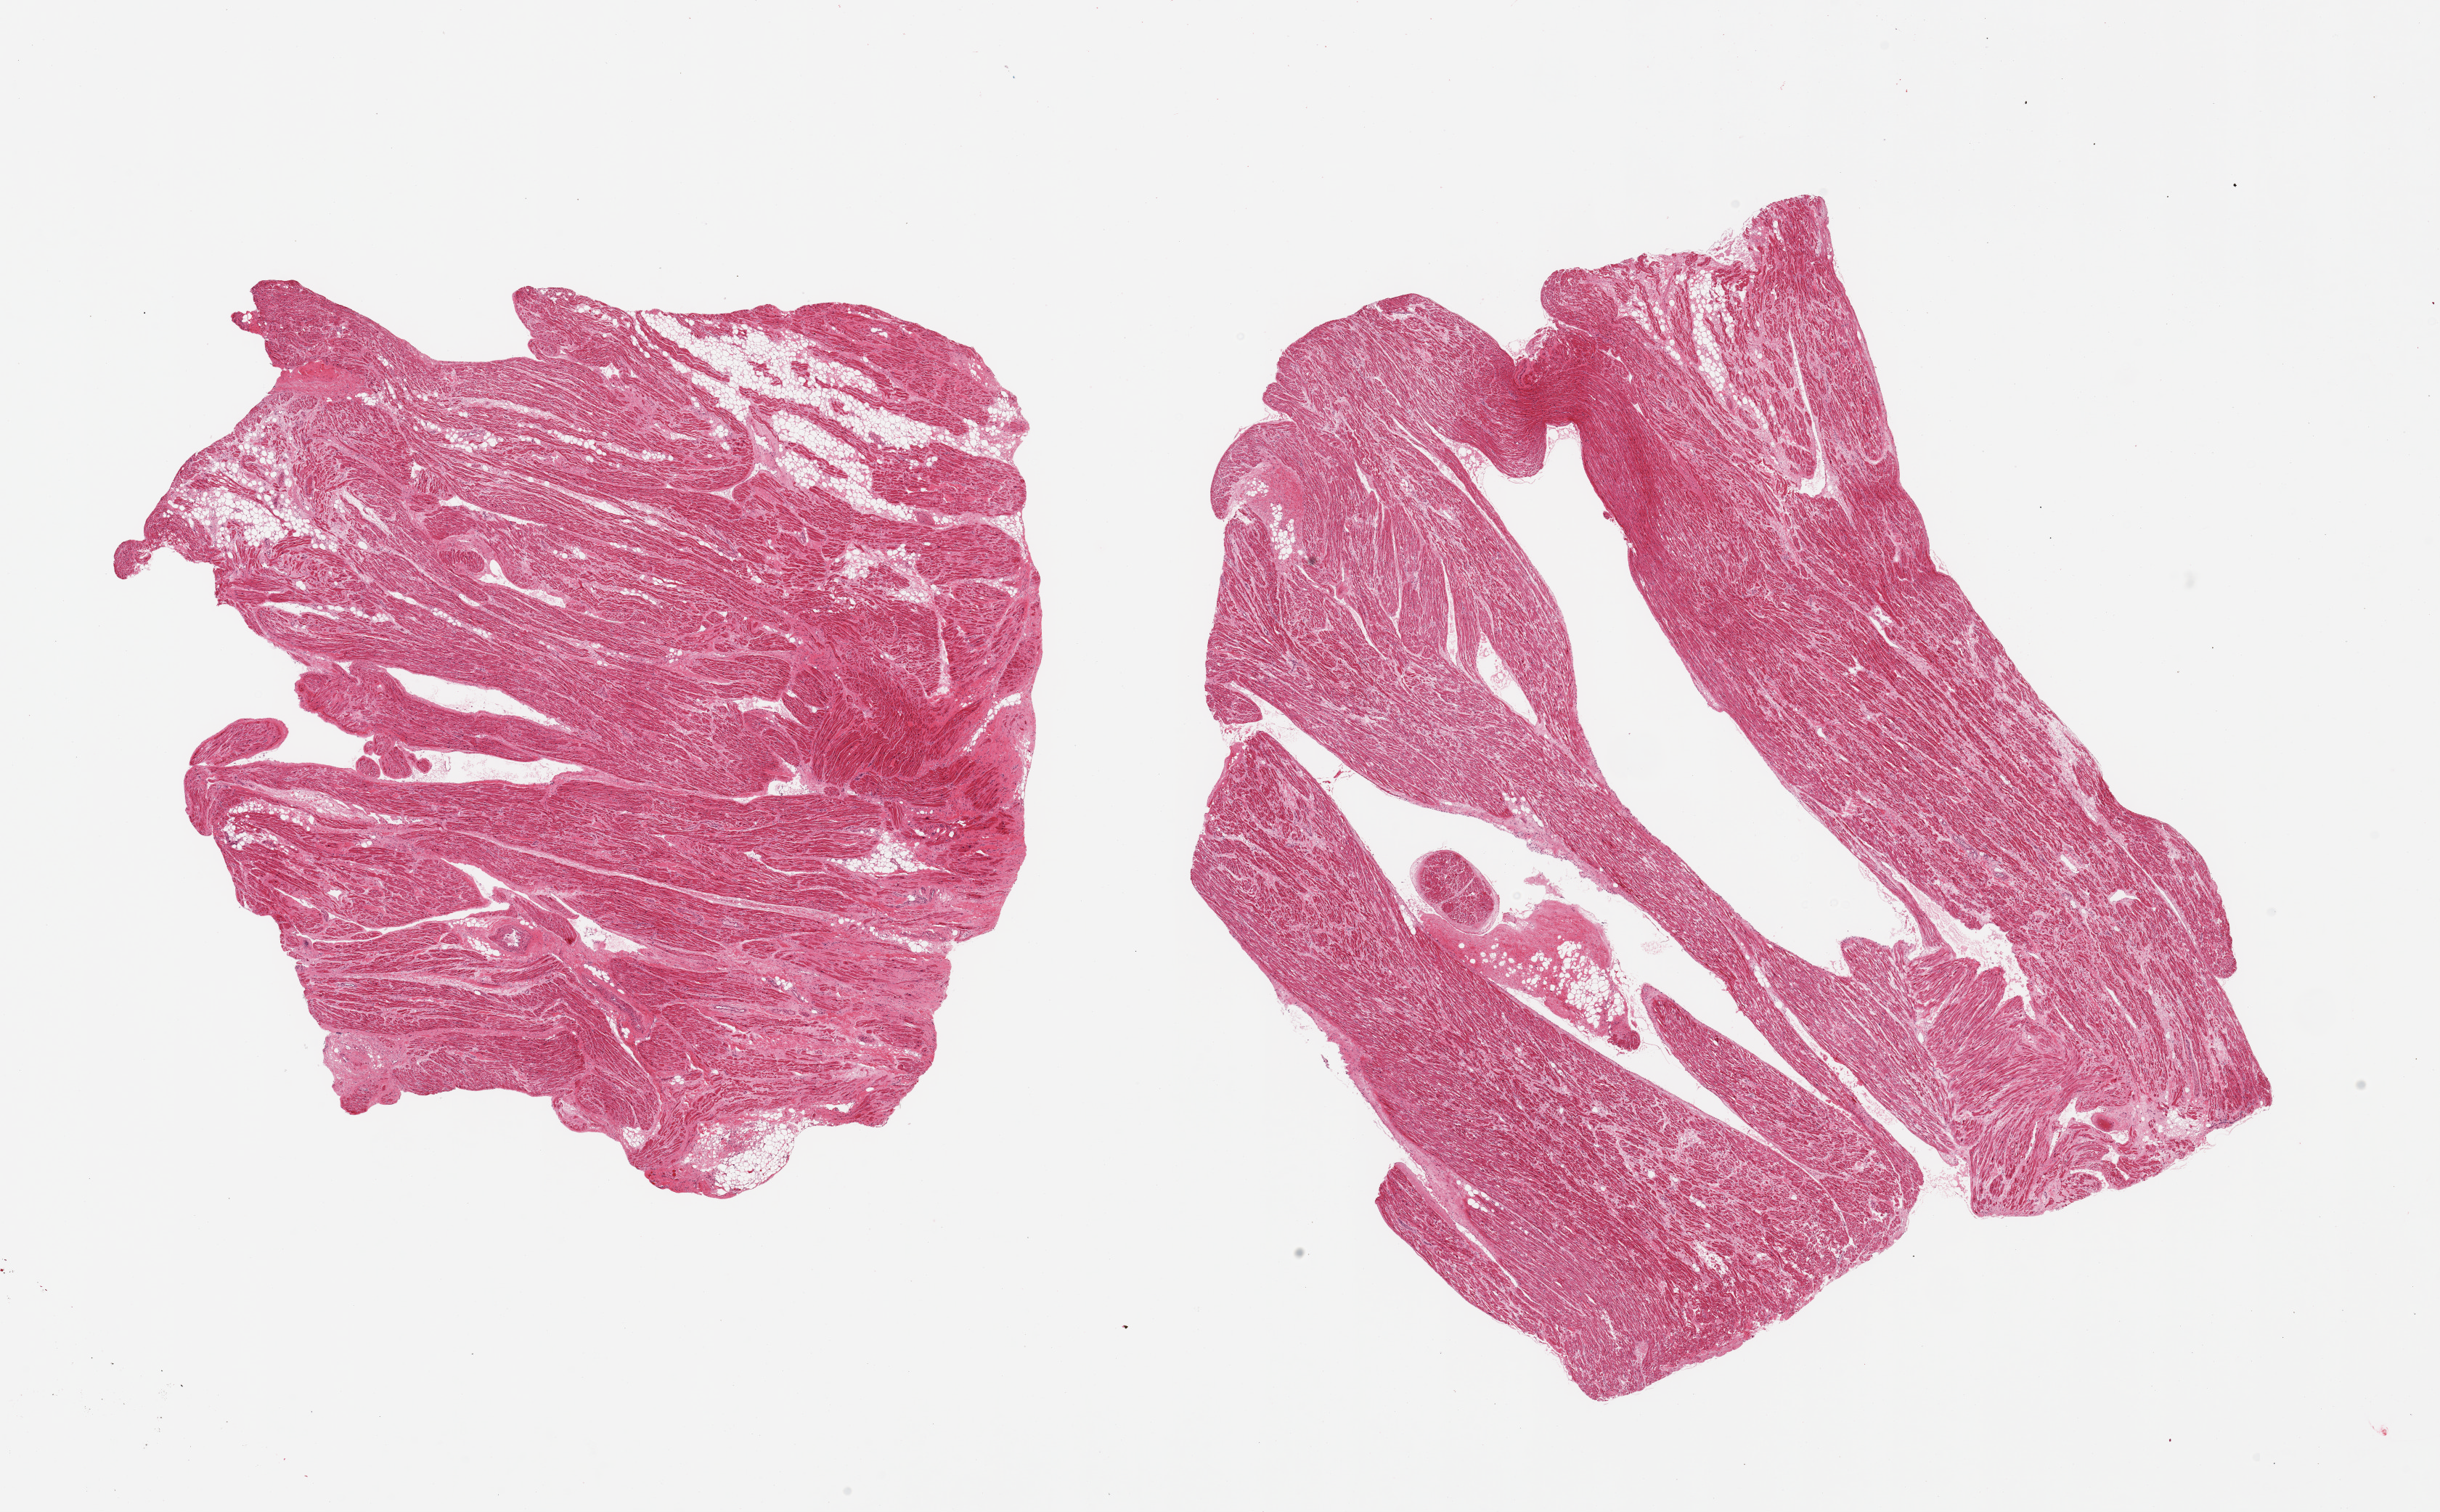
Hematoxylin and eosin (H&E) whole-slide image — low-resolution overview of the scanned area, about 26.6 x 16.5 mm (from a 20x scan). PAXgene-fixed, paraffin-embedded tissue. Target tissue: auricular appendage. Donor tissue sample. Donor: male.
Pathologist's review note for this sample: 2 pieces; fibromuscular tissue with ~10% internal/external fat.